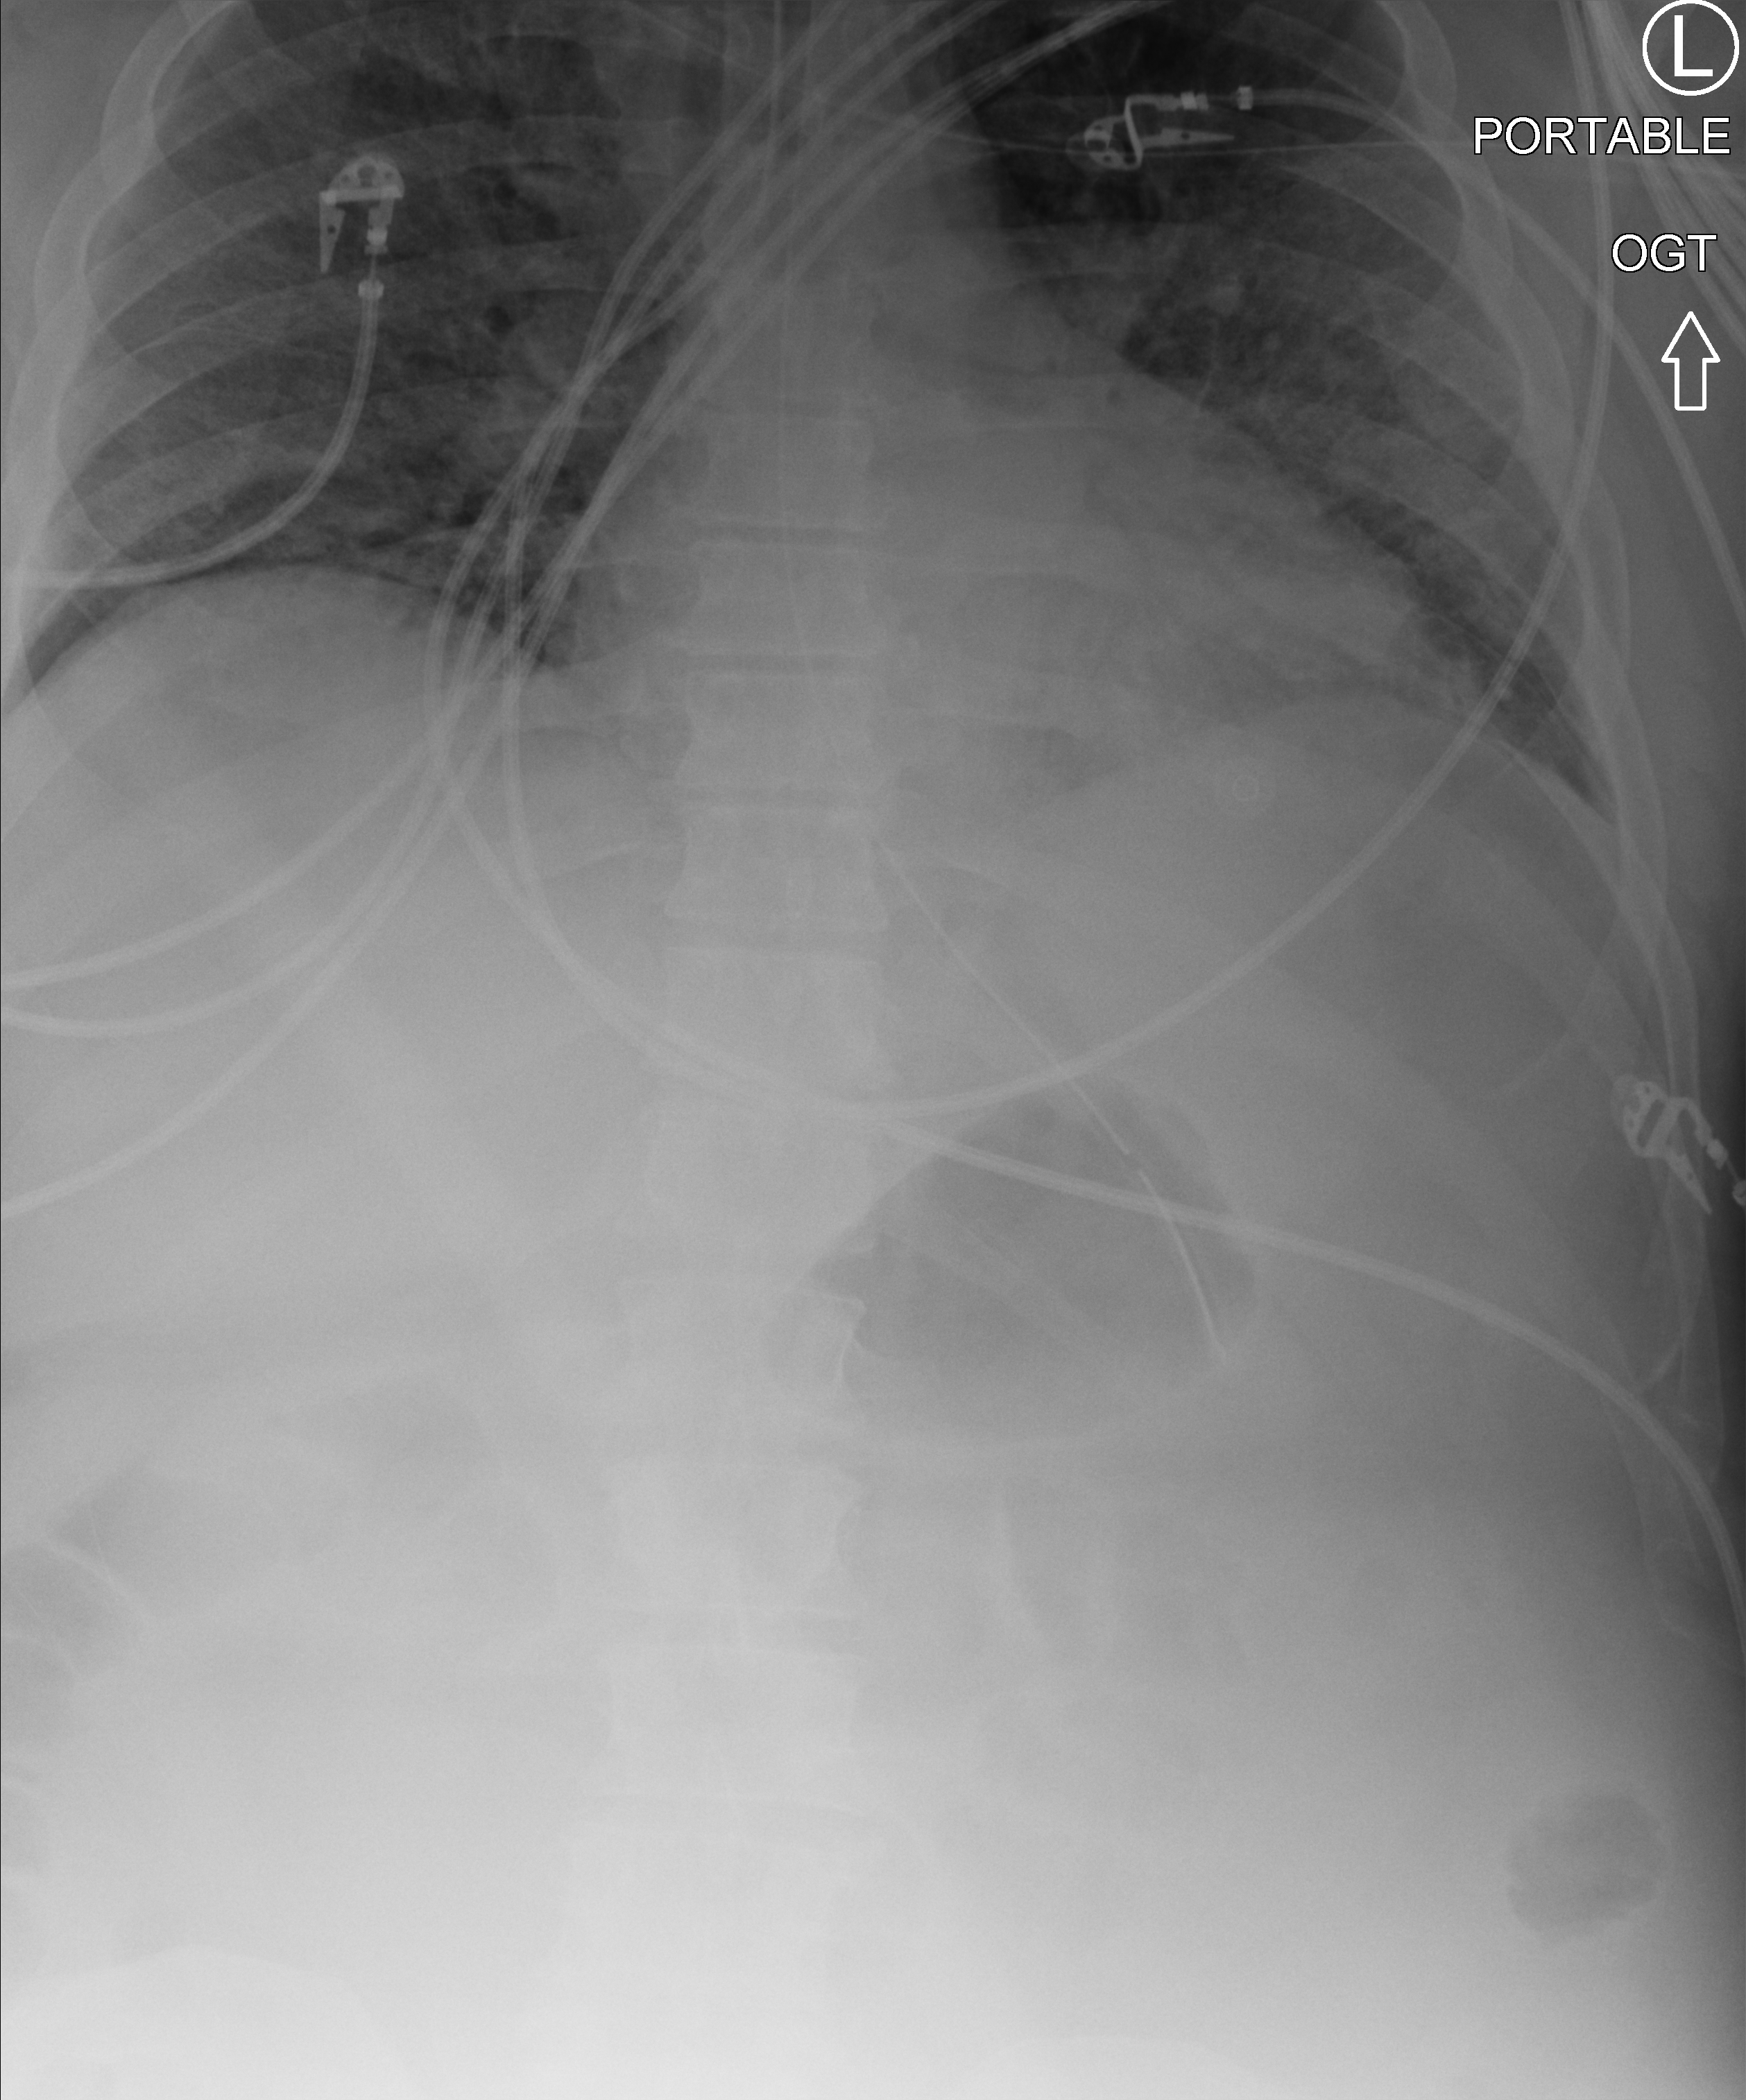
Chest X-ray (portable). Patient hospitalised with COVID-19; male, aged 18–59 years.
From the hospital-stay record, not from the radiograph (when in the stay this image was taken is not recorded): admitted to intensive care during this hospital stay: yes; hypertension (admission record): yes; mechanically ventilated during this hospital stay: yes.